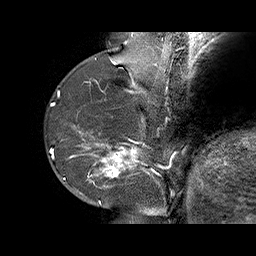
Breast MRI (dynamic contrast-enhanced), one sagittal slice. Slice 19 of 70 in the series (ordered by position). Dynamic contrast-enhanced series, time point 2 of 6 at this slice position (early post-contrast). 1.5 T. TE 4.5 ms, TR 32.4 ms. 256 × 256 image matrix. Female patient. Case-level facts recorded for this patient, not image findings: setting: breast cancer imaged before/during neoadjuvant chemotherapy; receptor status: HR-positive, HER2-negative.
Structures marked on this image (semi-automatically segmented with operator editing):
- analysis volume of interest (the breast-tissue region the enhancement analysis was run in; not a lesion): bounding box (x1, y1, x2, y2) in pixels: (71, 128, 159, 202)
- tumour enhancement mask (voxels above the 100 % enhancement threshold inside the analysis volume of interest): (71, 131, 156, 202)